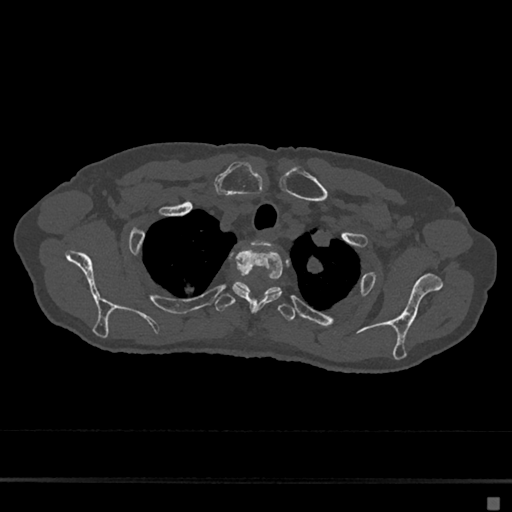
CT including the spine, one axial slice; position 565 of 797 along the scan axis; 120 kVp; bone window (W 1800 / L 400 HU); 0.5 mm slice thickness; 512 × 512 image matrix. Patient: female, 68 years. Case-level facts recorded for this patient, not image findings: primary cancer: renal.
Annotated regions visible in this slice (semi-automatic segmentation, software-assisted and operator-edited):
- T1 vertebra: bounding box [x1, y1, x2, y2] px = [253, 240, 272, 248]
- T2 vertebra: [232, 249, 283, 312]
- T3 vertebra: [215, 281, 296, 321]